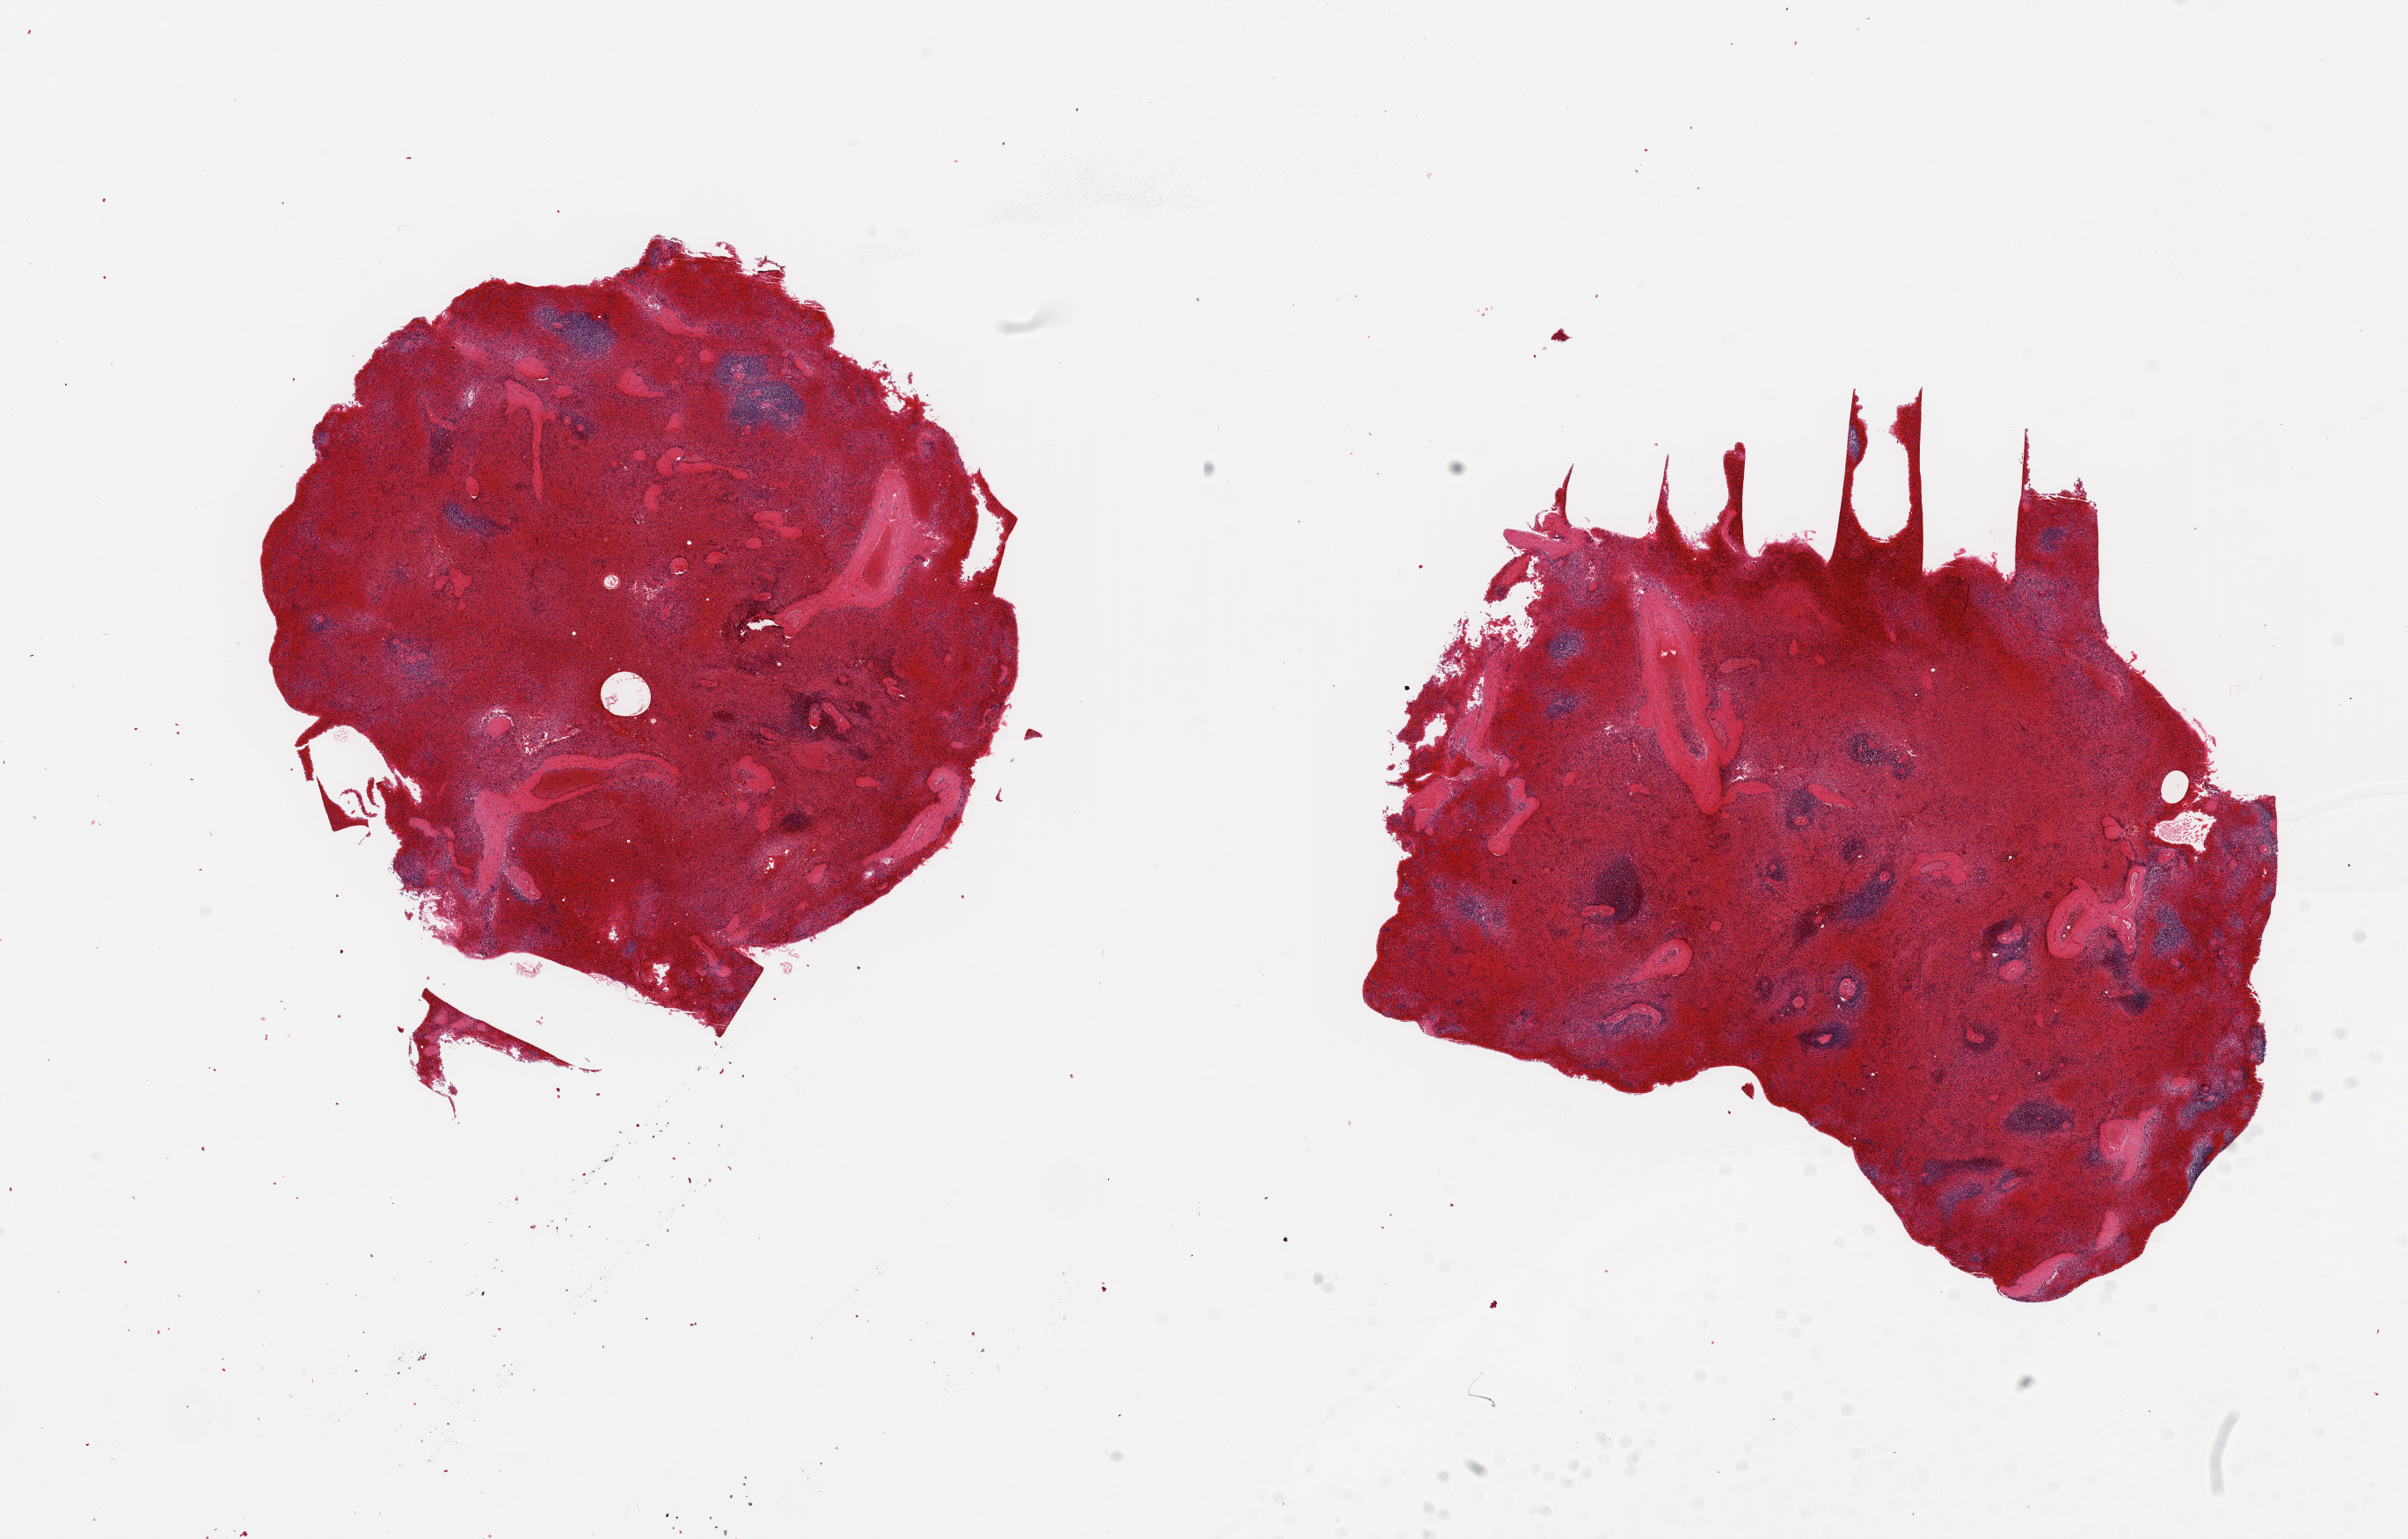
Digitized H&E-stained section, brightfield, whole scanned area (about 21.7 x 13.8 mm) shown as a low-resolution overview; PAXgene-fixed paraffin-embedded (PFPE) section; sampled site (target tissue): spleen; donor tissue sample. Male donor.
Reviewer comment on this tissue sample: 2 pieces ~7x6mm. Poorly preserved, moderate congestion.